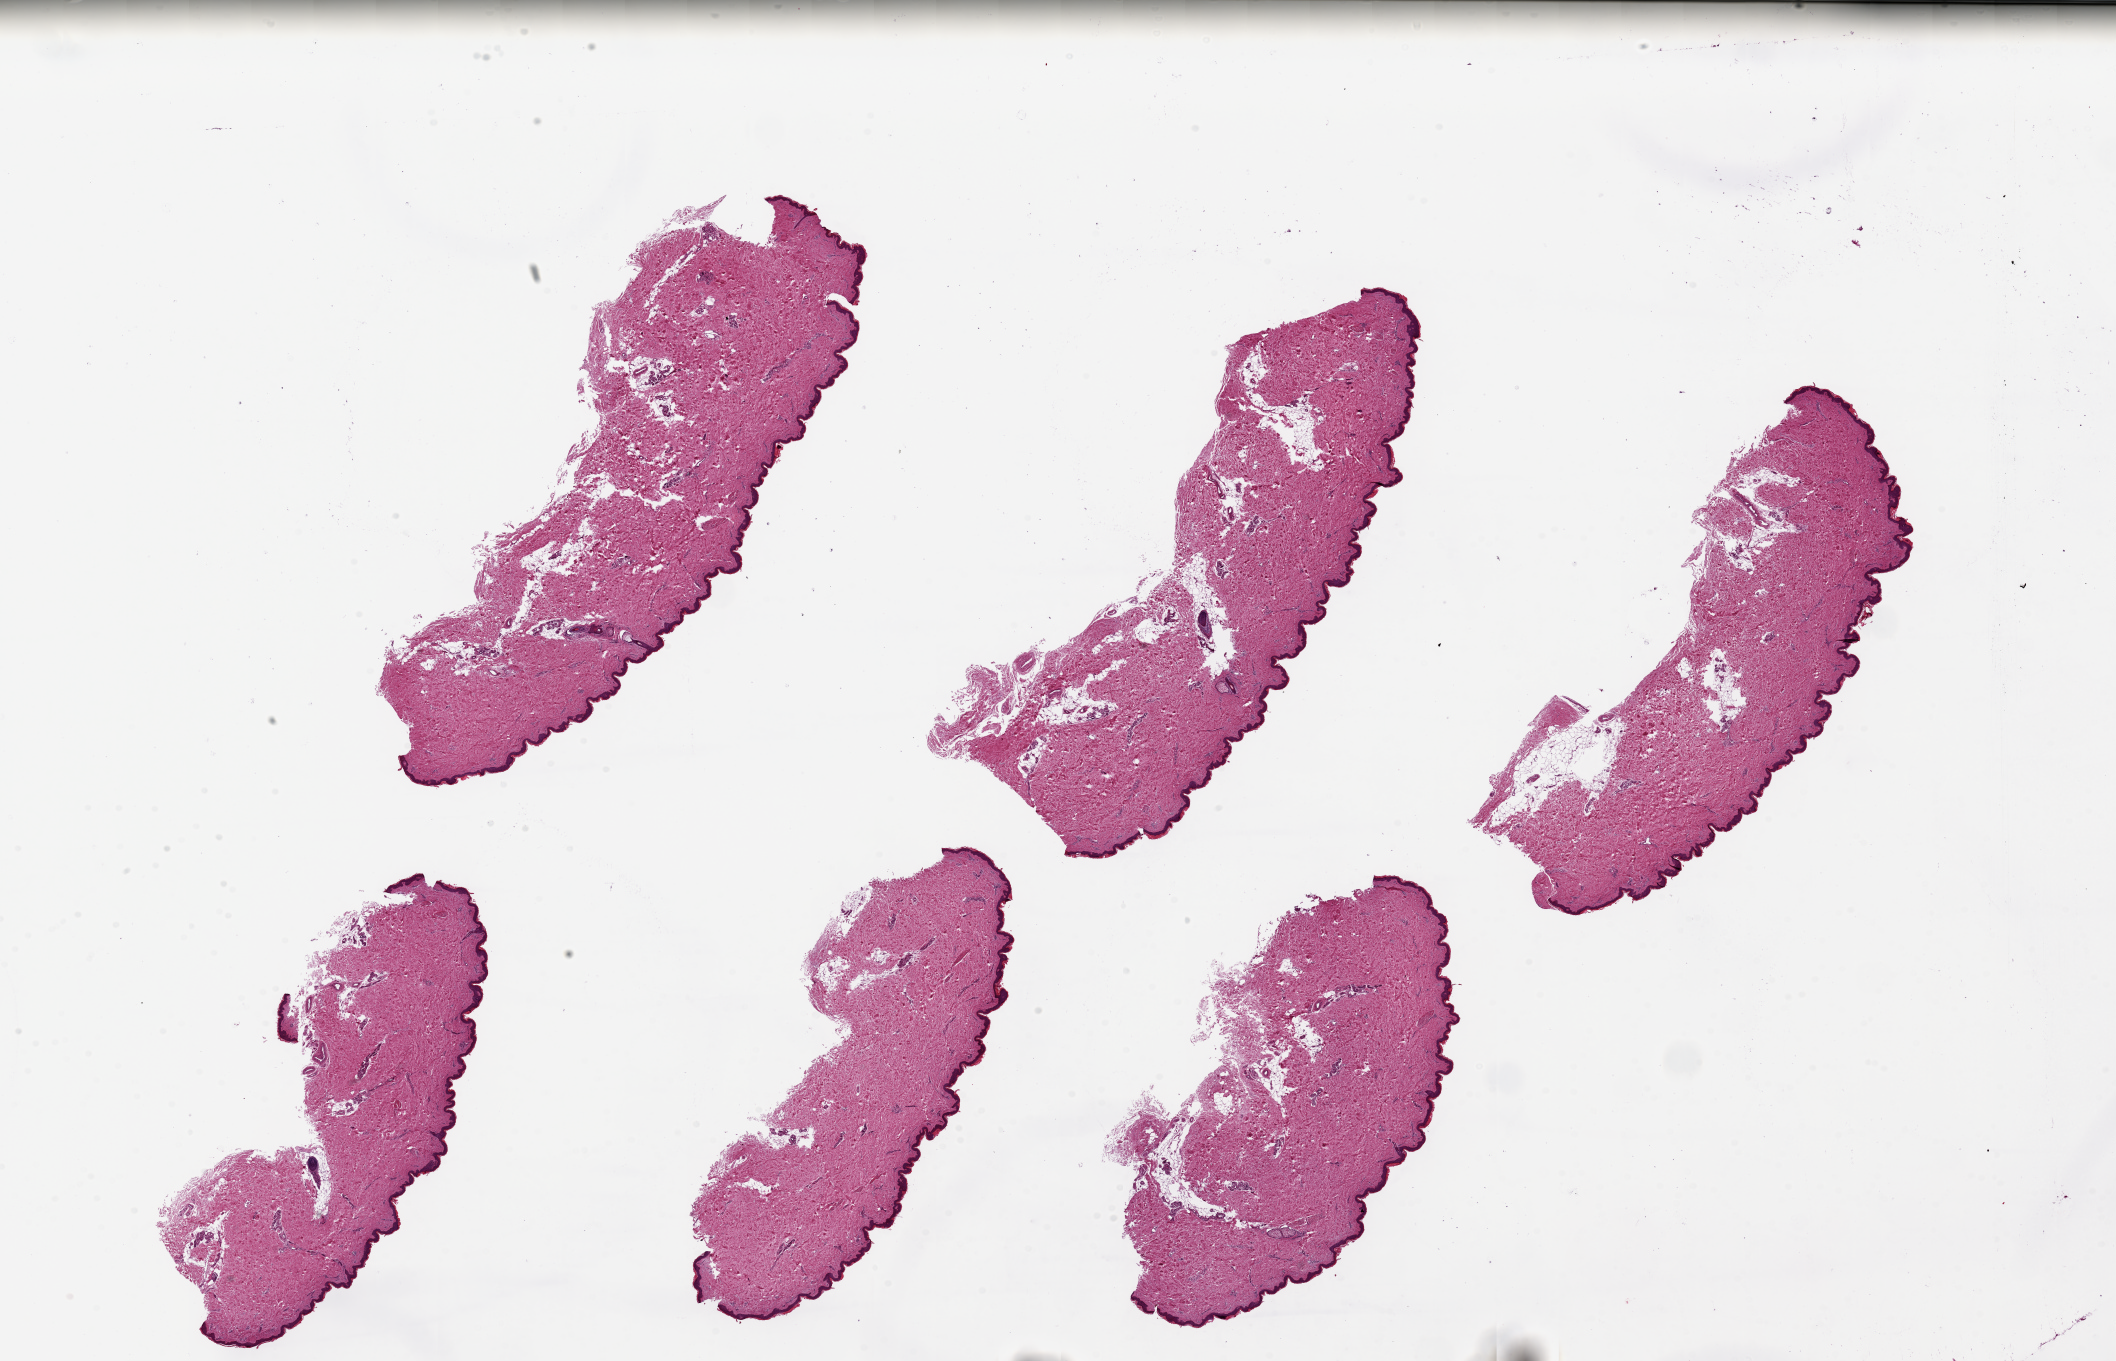
Digitized haematoxylin and eosin-stained section, brightfield — a low-resolution overview of the entire scanned area, about 33.5 x 21.5 mm. PAXgene-fixed, paraffin-embedded tissue. Section of skin of lower leg (target tissue). Donor tissue sample. Donor: female.
Reviewer comment on this tissue sample: 6 pieces, up to 11x4mm; well trimmed without subcutaneous adipose.